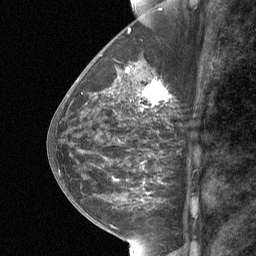
Breast MRI (dynamic contrast-enhanced), one sagittal slice; position 29 of 64 along the scan axis; dynamic contrast-enhanced study with each time point stored as its own series, time point 2 of 3 at this slice position (early post-contrast, ordered by acquisition time); 1.5 T; TE 4.8 ms, TR 27 ms; 2 mm slice thickness; 256 × 256 image matrix, field of view 180 × 180 mm. Female patient, age 59 years. Case-level facts recorded for this patient, not image findings: setting: breast cancer imaged before/during neoadjuvant chemotherapy; receptor status: triple-negative.
Annotated regions visible in this slice (semi-automatic segmentation, software-assisted and operator-edited):
- analysis volume of interest (the breast-tissue region the enhancement analysis was run in; not a lesion): bounding box <127,66,171,122> (left, top, right, bottom; pixels)
- tumour enhancement mask (voxels above the 90 % enhancement threshold inside the analysis volume of interest): <142,80,167,103>